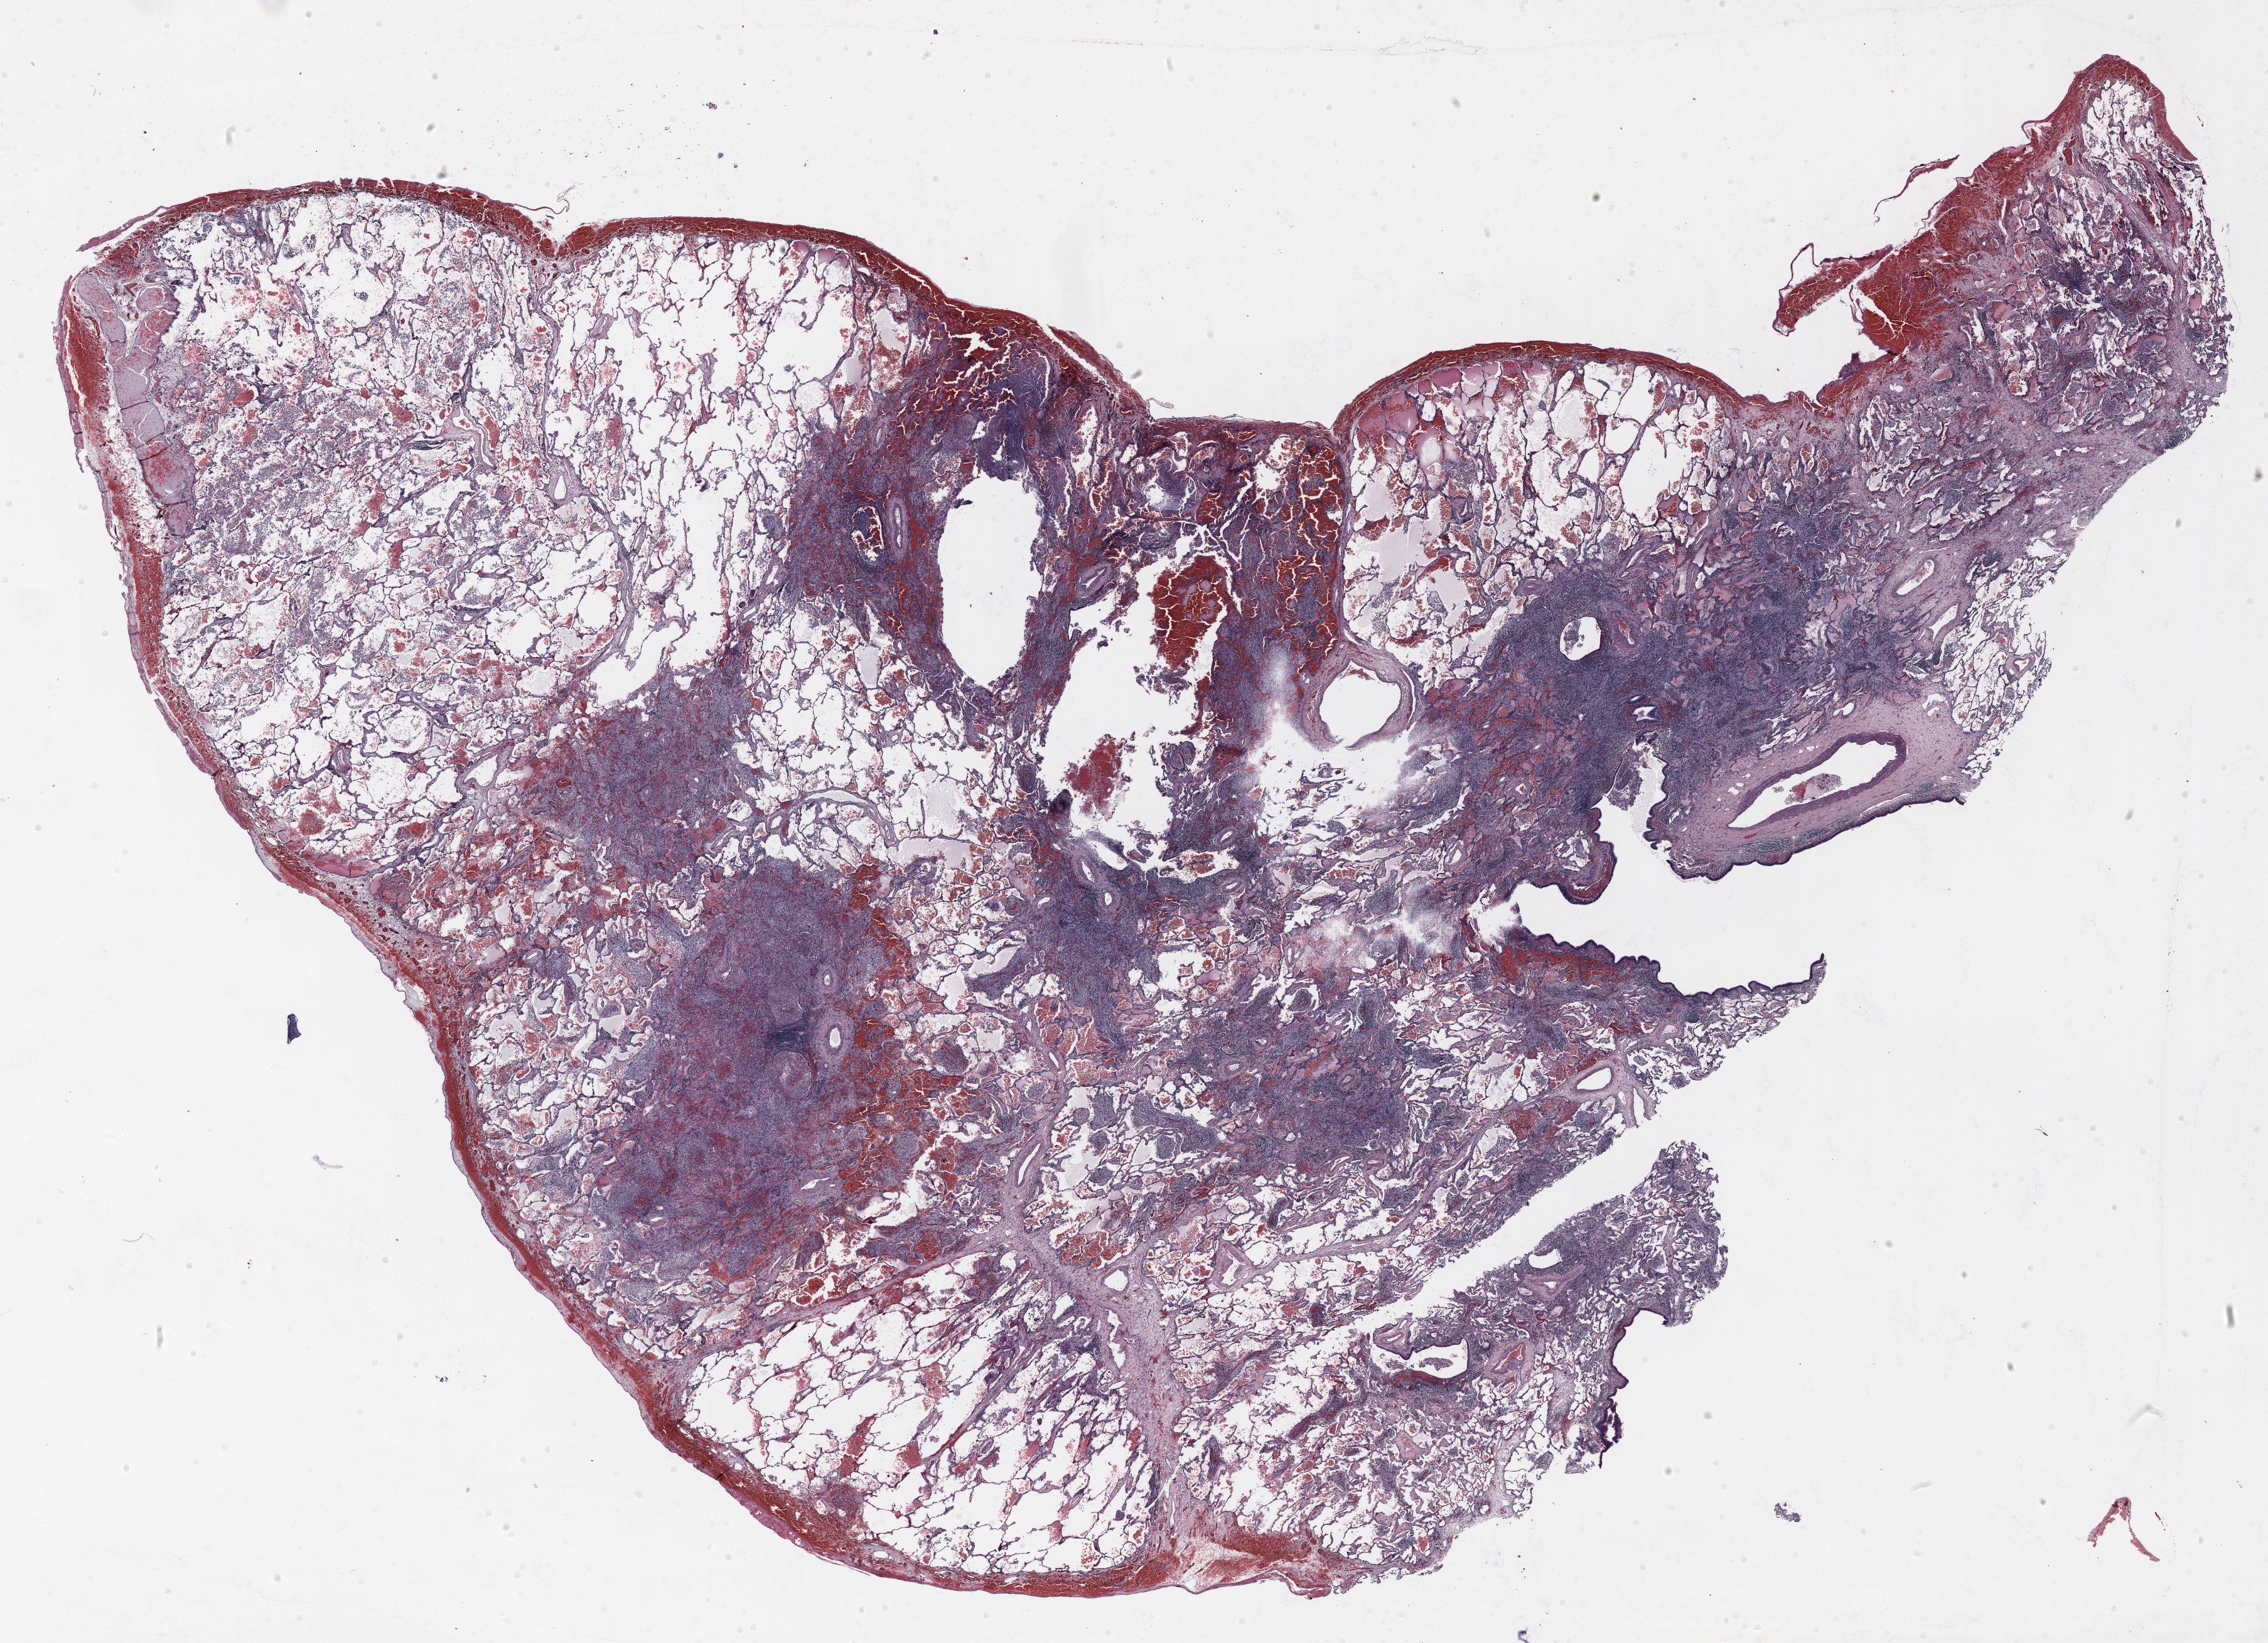
H&E whole-slide image, a low-resolution overview of the entire scanned area, about 29.0 x 21.0 mm. Formalin-fixed paraffin-embedded (FFPE) section. Lung tissue. Male, age 70 at enrolment. Current smoker at enrolment. Grade: poorly differentiated (G3).
* participant's lung-cancer diagnosis: Squamous cell carcinoma, NOS (ICD-O-3 8070/3)
* stage (AJCC 6th edition): IB
* ICD-O-3 topography: upper lobe of lung (C34.1)
* tumour size (pathology): 47 mm
* primary tumour location (clinical record): left upper lobe